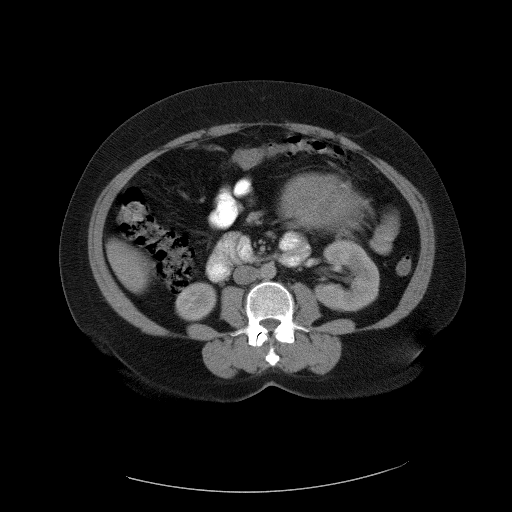
Contrast-enhanced abdominal CT, one axial slice. Slice 52 of 90 in the series (ordered by position). Reconstruction kernel FC01. 120 kVp. Soft-tissue window (W 400 / L 40 HU). 512 × 512 image matrix, field of view 480 × 480 mm. Patient: female, 55 years. Case-level facts recorded for this patient, not image findings: diagnosis: adrenocortical carcinoma; tumour side: left adrenal; tumour size at pathology: 22 cm; Ki-67 index: 10 %; stage (as recorded): 3.
Structures marked on this image (semi-automatically segmented with operator editing):
- mass: bounding box (x1, y1, x2, y2) in pixels: (280, 175, 370, 236)